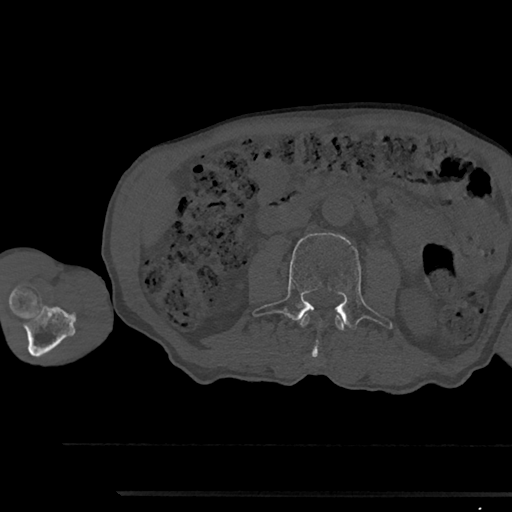
CT including the spine, one axial slice. Position 503 of 797 along the scan axis. Reconstruction kernel Br40s/3. Bone window (W 1800 / L 400 HU). 0.5 mm slice thickness. 512 × 512 image matrix, field of view 367 × 367 mm. Patient: male, 79 years. Case-level facts recorded for this patient, not image findings: primary cancer: prostate.
Annotated regions visible in this slice (semi-automatically segmented with operator editing):
- L2 vertebra: bounding box <300,316,344,330> (left, top, right, bottom; pixels)
- L3 vertebra: <253,233,393,357>